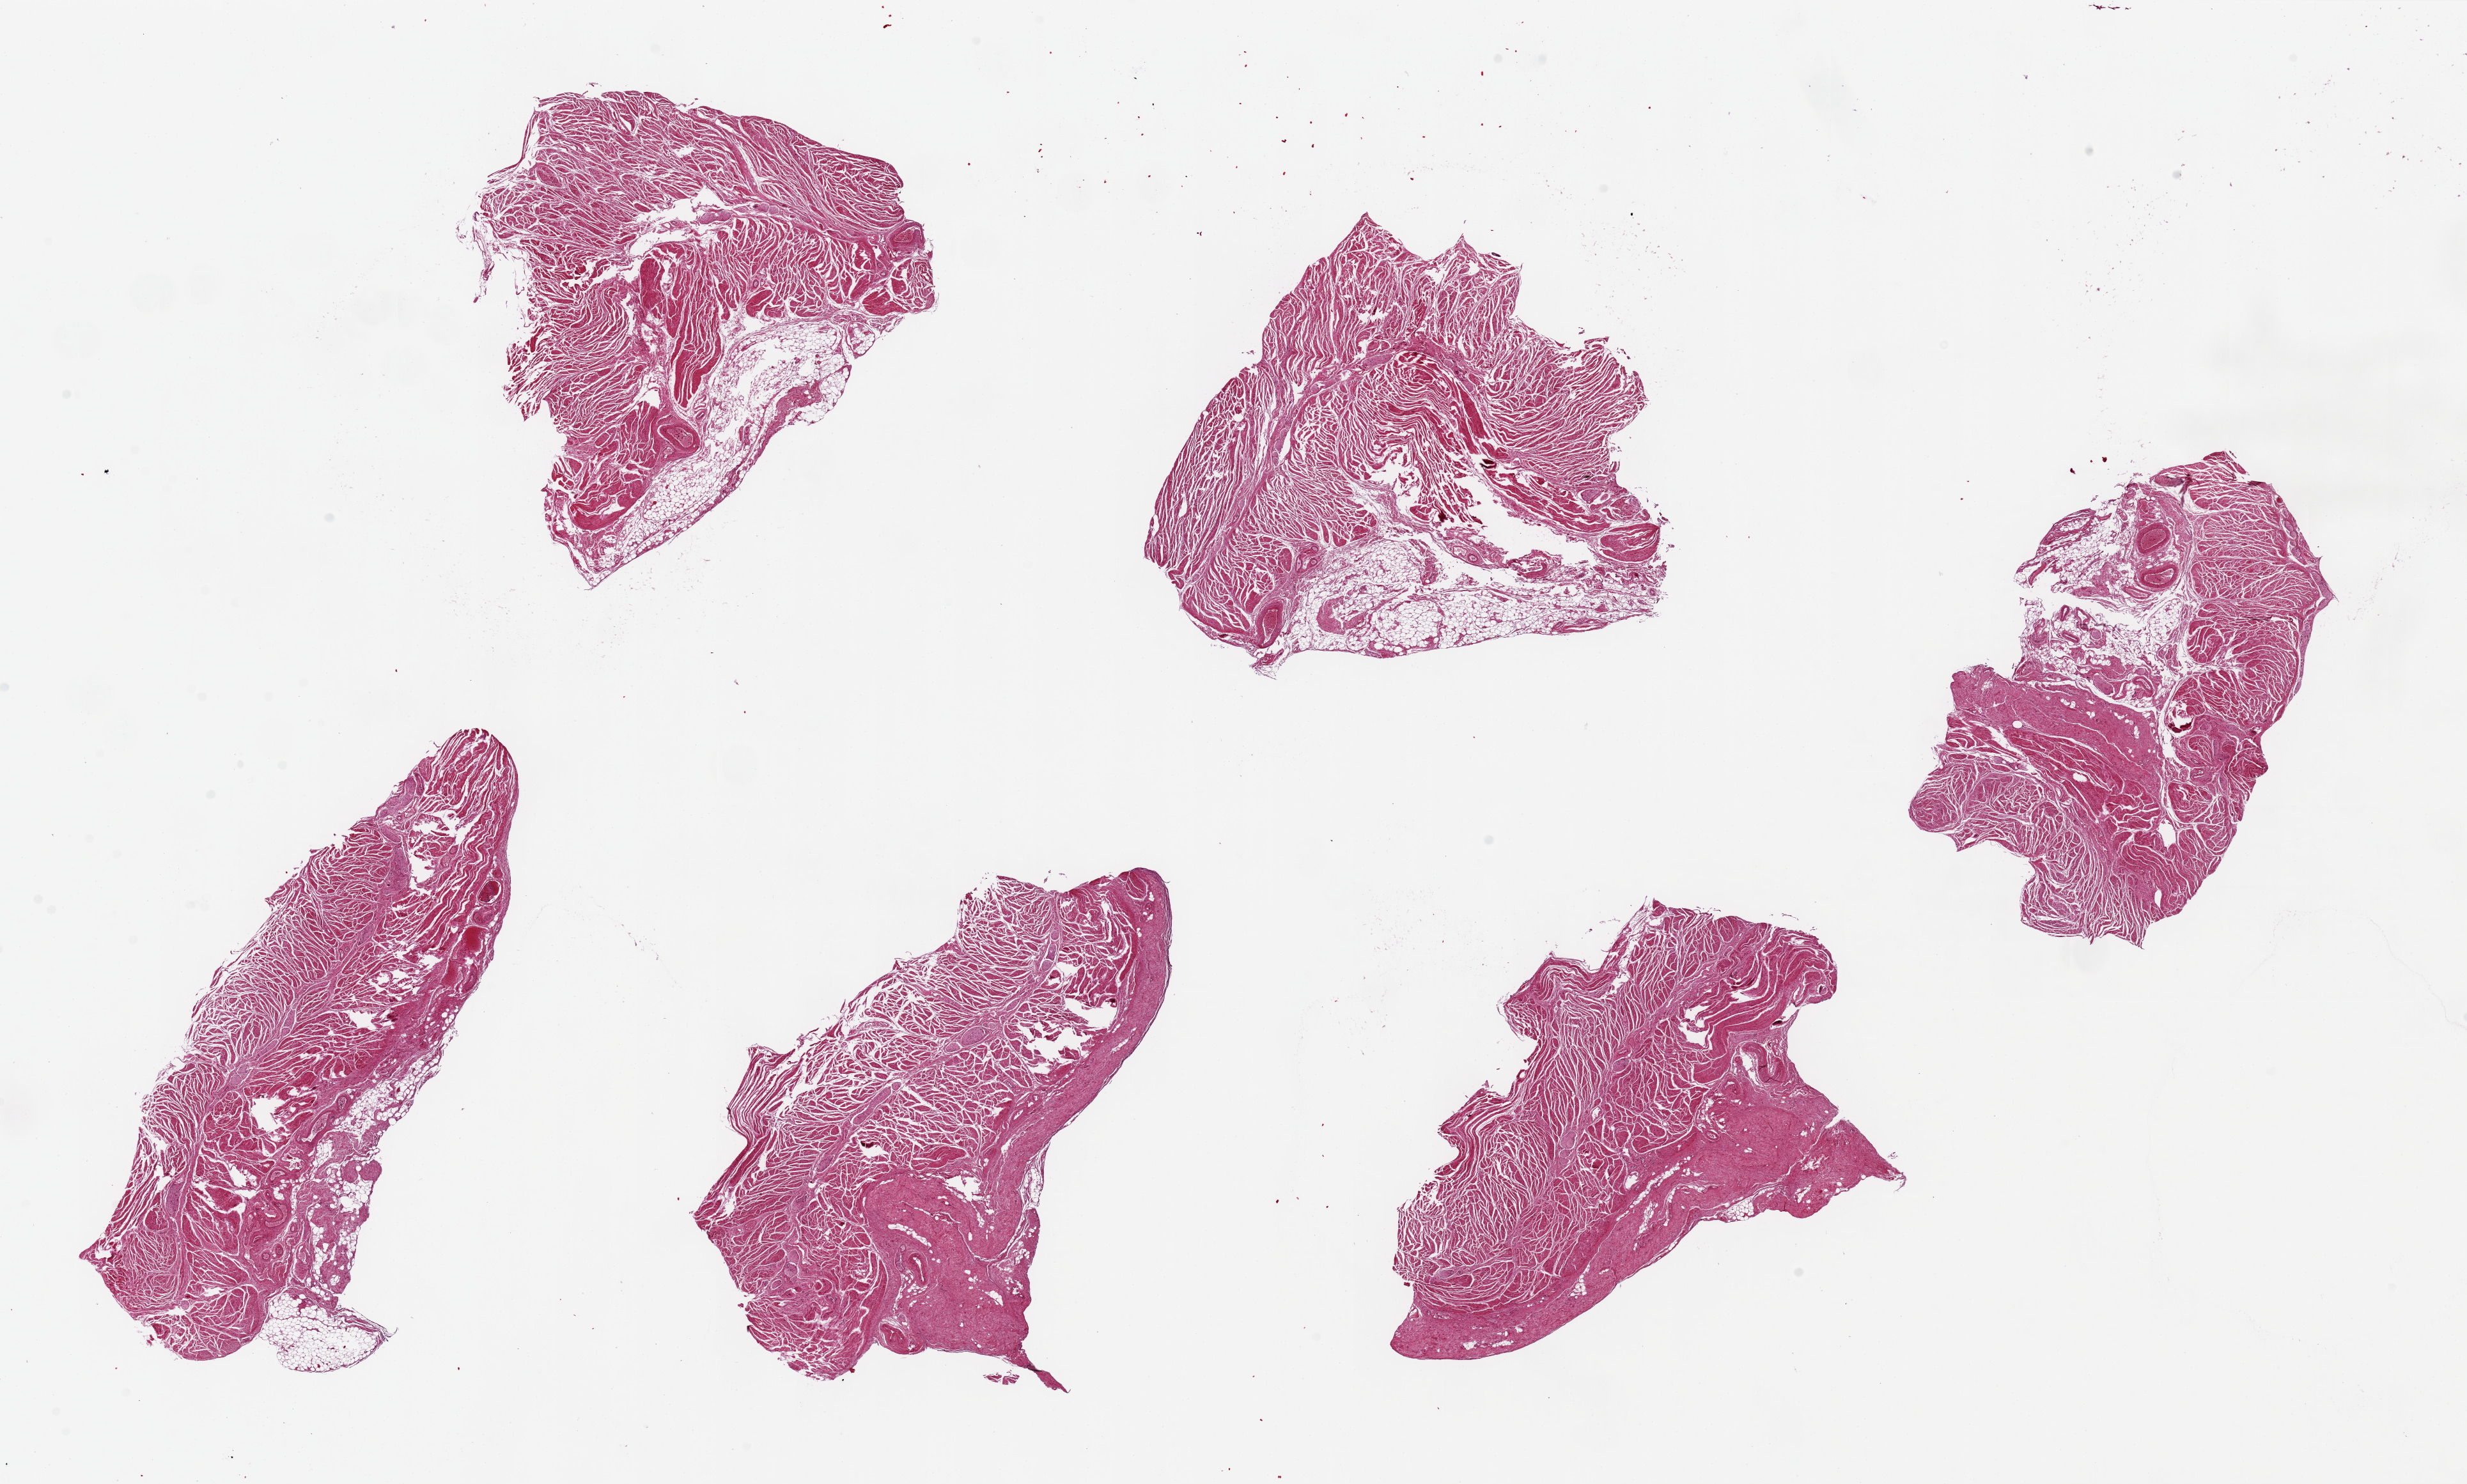
H&E whole-slide image — low-resolution overview of the scanned area, about 30.5 x 18.4 mm (slide scanned at 20x). PAXgene-fixed paraffin-embedded (PFPE) section. Sampled site (target tissue): gastroesophageal junction. Tissue donor sample. Donor: male.
Review note (as recorded): 6 pieces, up to 9x4mm; Muscle with outer bands of adipose tissue up to 1.5 mm thick (should be trimmed of adipose).